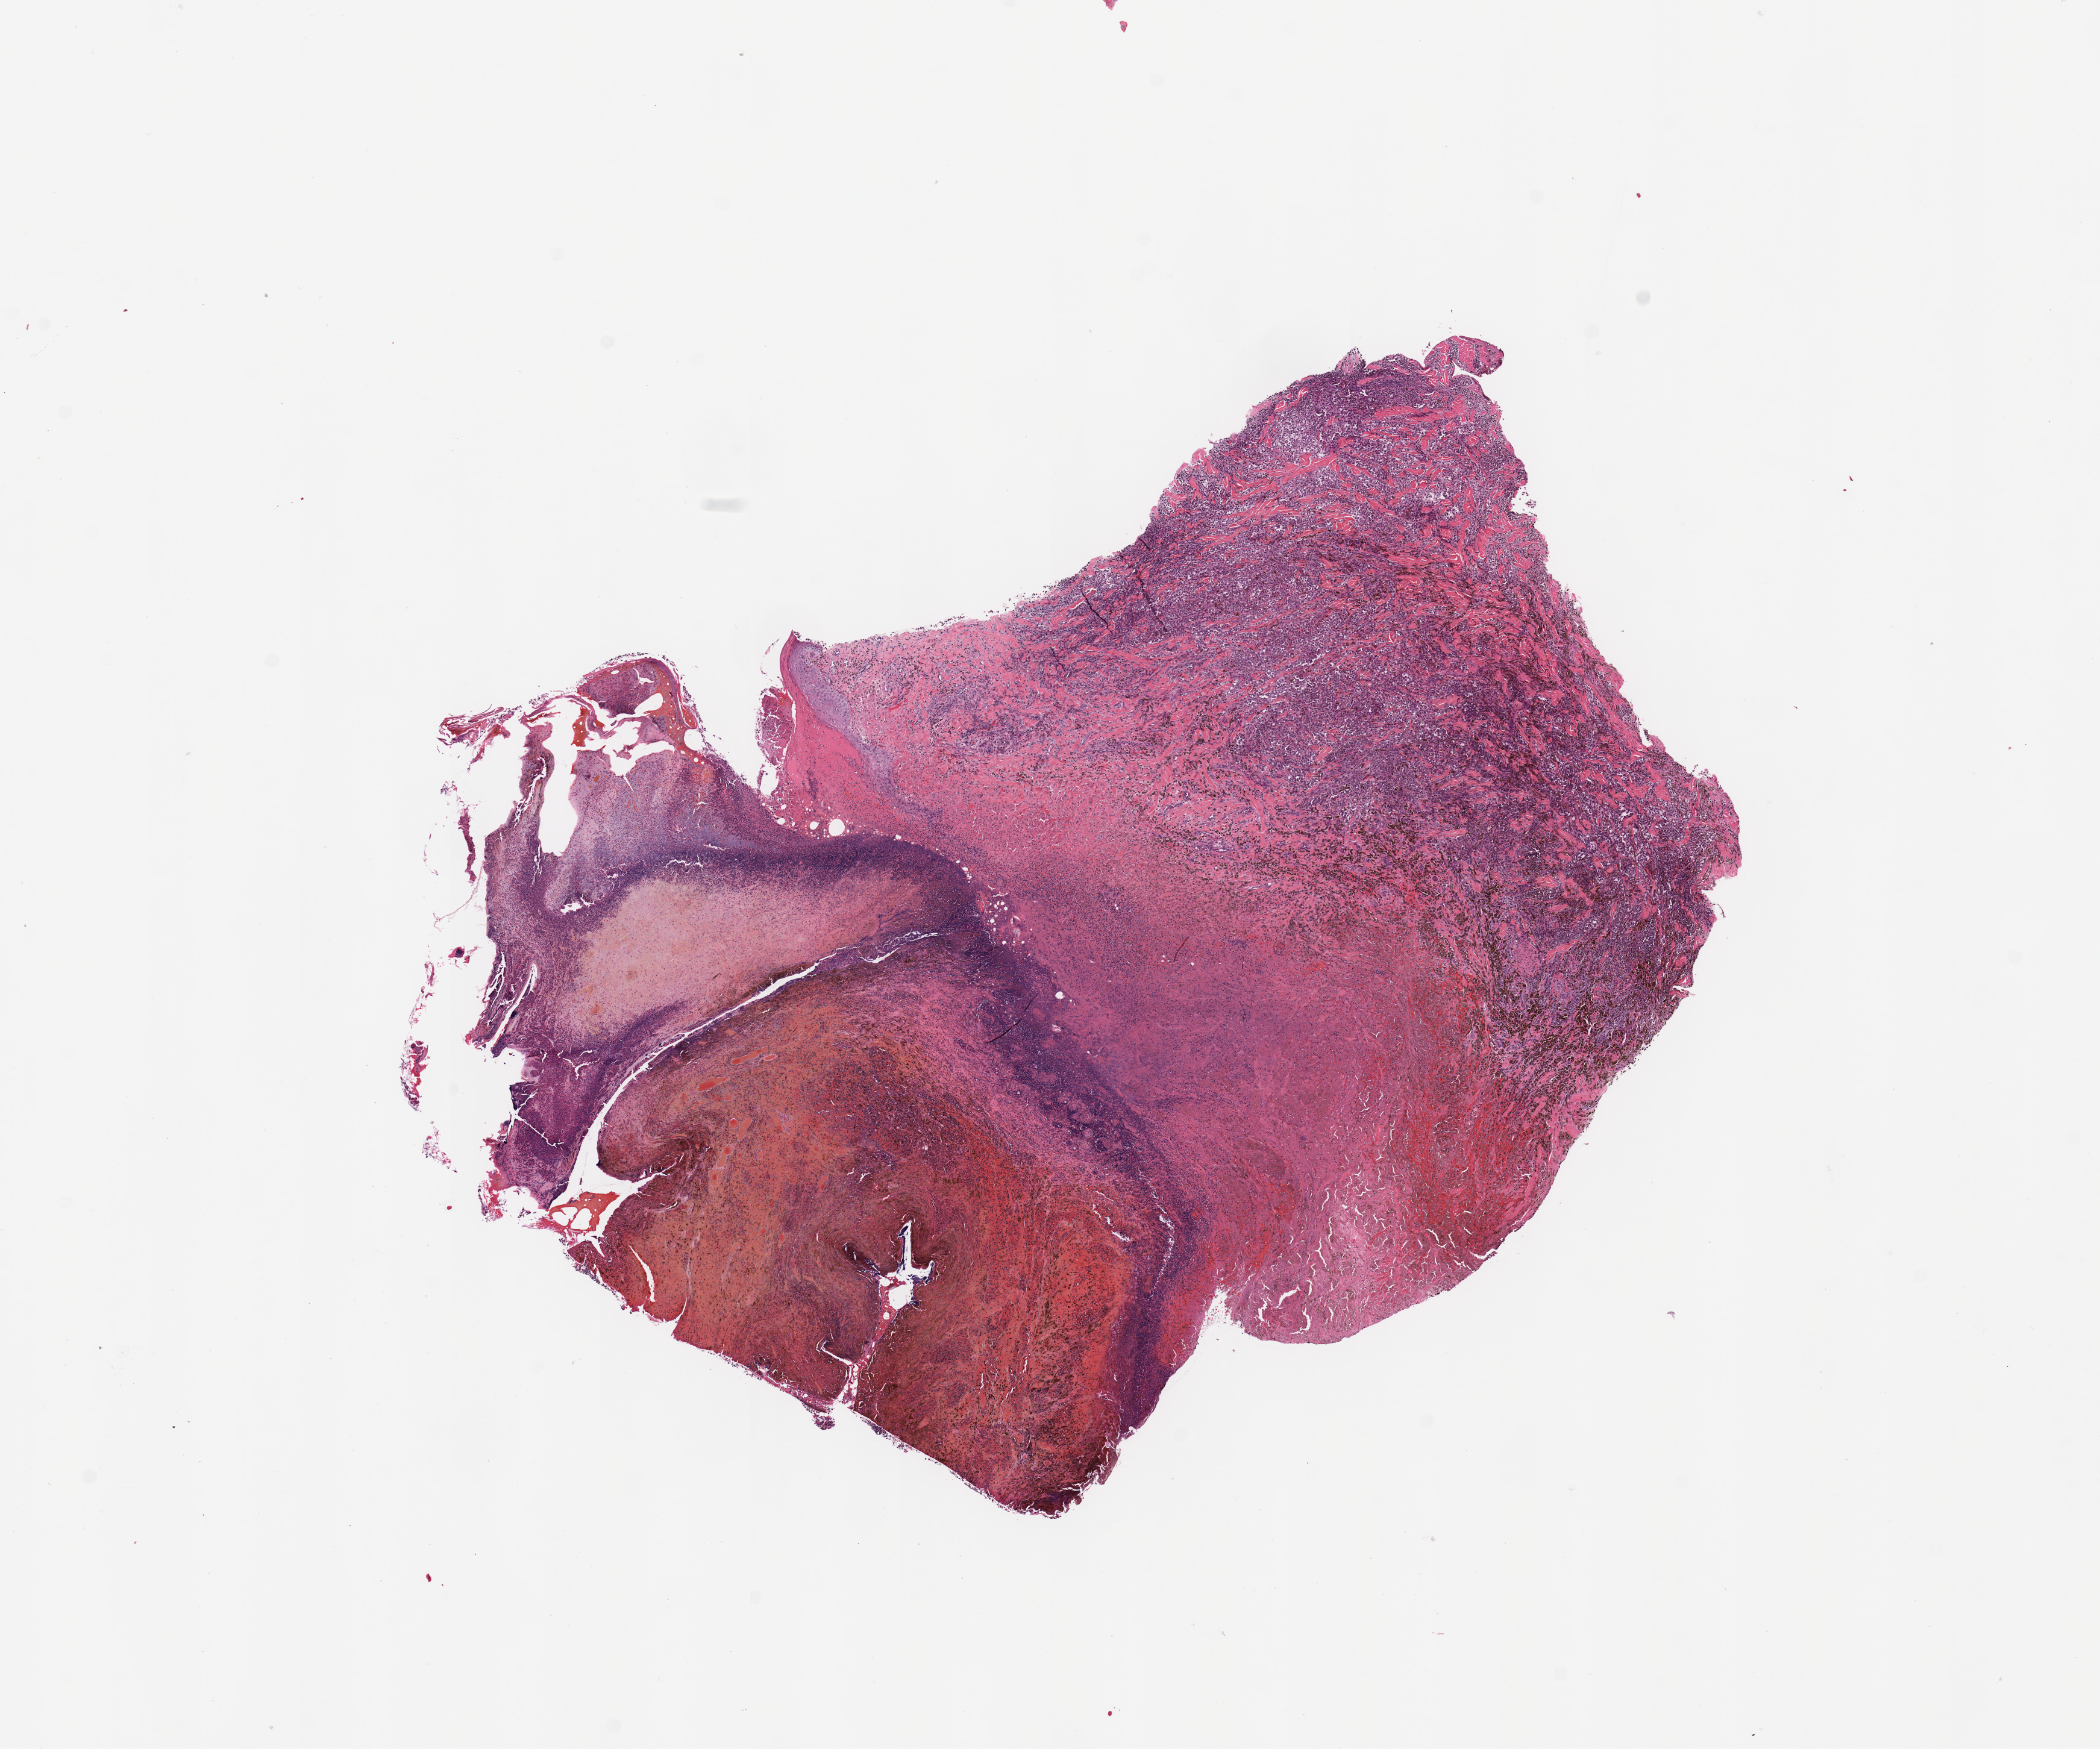
Hematoxylin and eosin (H&E) stained whole-slide image — a low-resolution overview of the entire scanned area, about 13.8 x 11.5 mm (slide scanned at 20x); melanoma tumour tissue; sampled site not recorded. Female, 69 y/o.
* diagnosis: Malignant melanoma, NOS
* primary tumour site (as recorded): trunk
* AJCC pathologic stage: IIIB